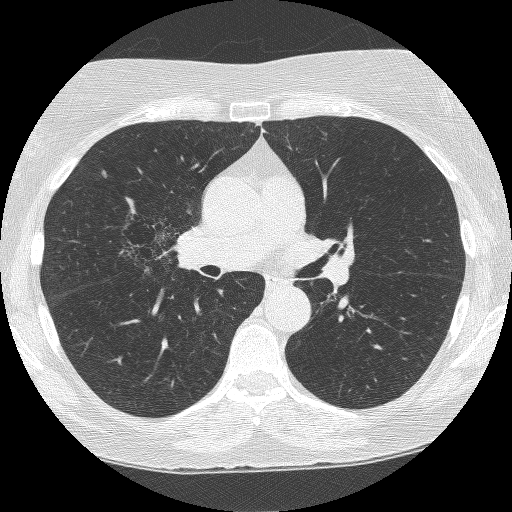
Low-dose screening chest CT, axial slice. Second screening round (one year after baseline). Lung window (W 1500 / L -600 HU). 1.25 mm slice thickness. Slice 140 of 249 in the series. Female, age 64 years at enrolment.
Expert-annotated lung lesion, bounding box [x1, y1, x2, y2] px = [117, 206, 202, 287]. The screening reader recorded 4 non-calcified nodules or masses ≥4 mm on this exam (right upper lobe, right upper lobe, right upper lobe, left upper lobe); which of them this box marks is not recorded.